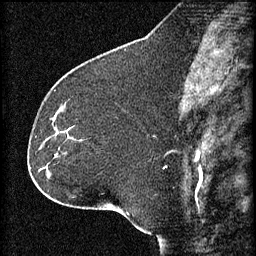
Breast MRI (dynamic contrast-enhanced), one sagittal slice. 3 images stored at this slice position (order not interpretable as contrast timing). 1.5 T. TE 4.2 ms, TR 8.2 ms. 2 mm slice thickness. 256 × 256 image matrix, field of view 180 × 180 mm. Patient: female, 32 years.
Structures marked on this image (semi-automatic segmentation, software-assisted and operator-edited):
- analysis volume of interest (the breast-tissue region the enhancement analysis was run in; not a lesion): bounding box [x1, y1, x2, y2] px = [47, 114, 84, 157]
- tumour enhancement mask (voxels above the 70 % enhancement threshold inside the analysis volume of interest): [57, 132, 59, 135]